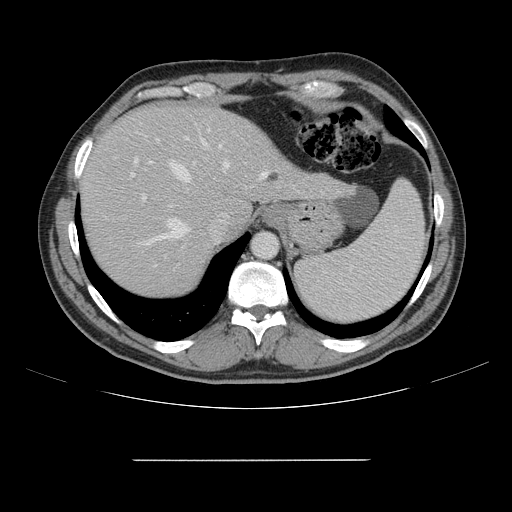
Contrast-enhanced abdominal CT, one axial slice. Position 122 of 164 along the scan axis. 120 kVp. Intravenous contrast given. Soft-tissue window (W 400 / L 40 HU). 2.5 mm slice thickness. 512 × 512 image matrix, field of view 404 × 404 mm. Male patient, age 54 years. Case-level facts recorded for this patient, not image findings: diagnosis: colorectal cancer liver metastases, imaged before liver resection; multiple liver metastases: yes; largest metastasis: 1 cm.
Annotated regions visible in this slice (expert manual segmentation):
- hepatic veins: bounding box (x1, y1, x2, y2) in pixels: (141, 139, 268, 245)
- liver: (82, 106, 342, 295)
- planned liver remnant (the part of the liver to remain after resection): (81, 106, 254, 295)
- portal vein (with intrahepatic branches): (115, 137, 225, 272)
- liver metastasis: (269, 174, 279, 182)